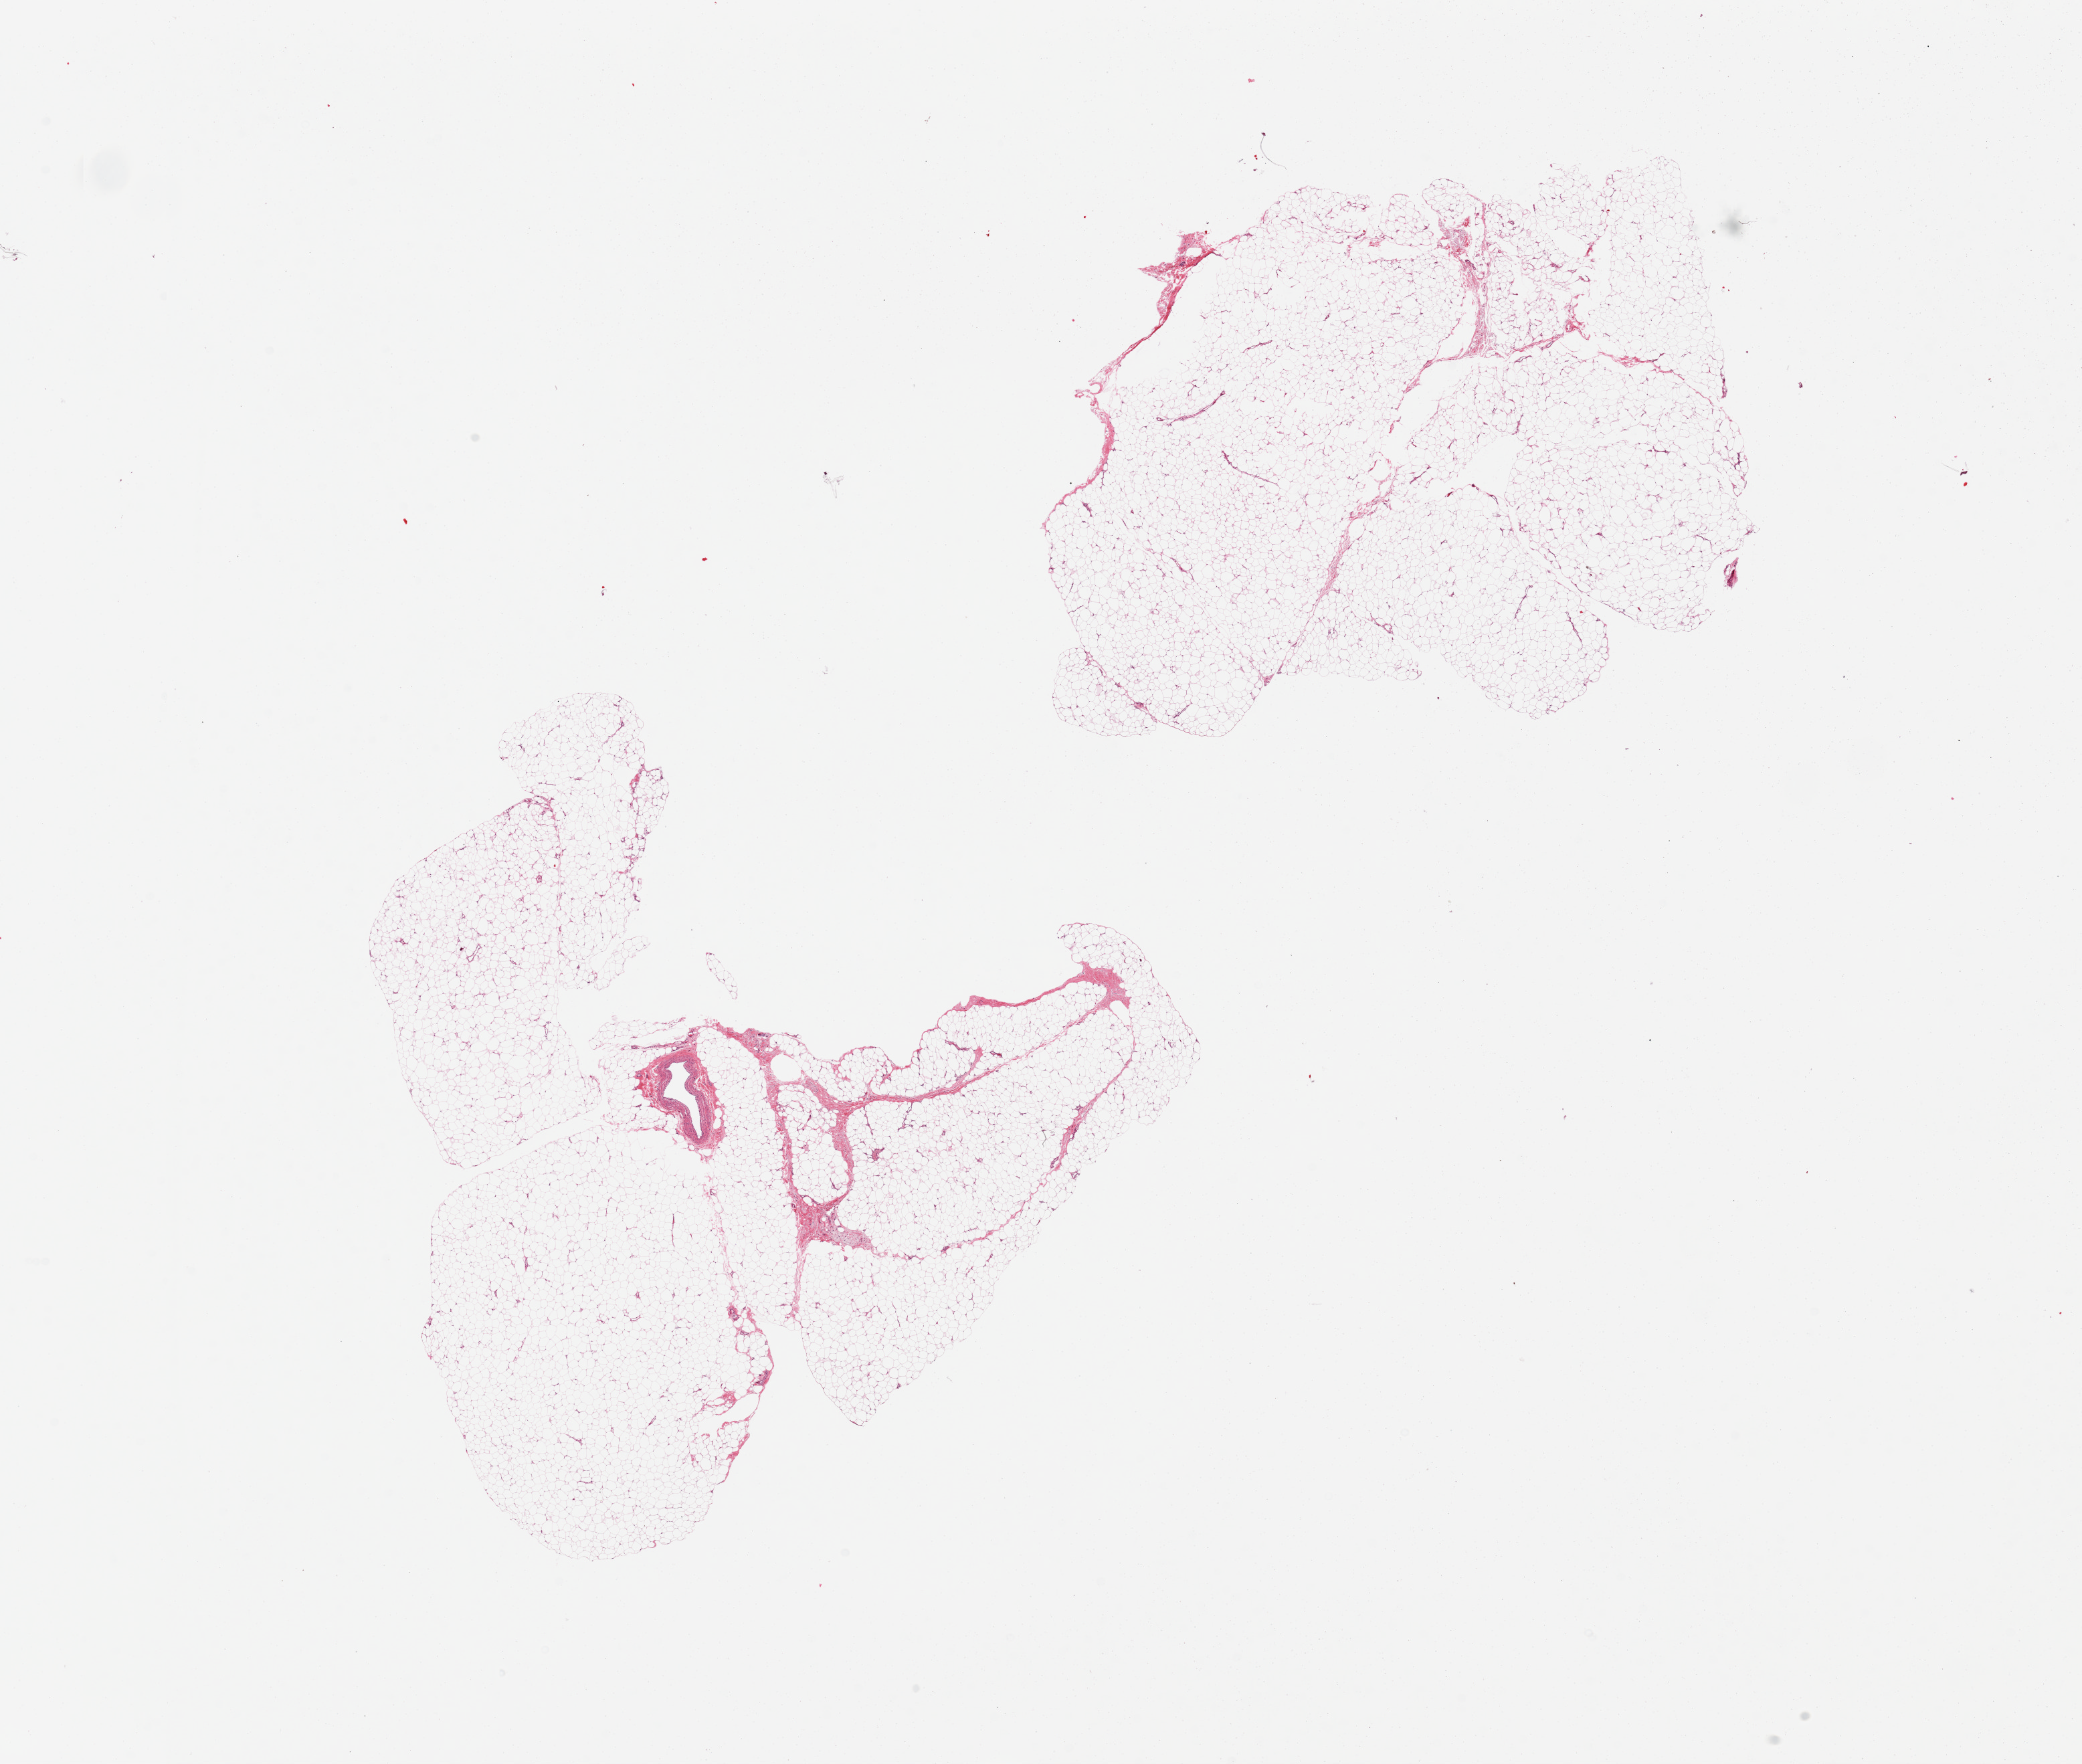
Hematoxylin and eosin (H&E) whole-slide image, brightfield — whole scanned area (about 24.6 x 20.9 mm, acquisition: 20x scan) shown as a low-resolution overview, PAXgene-fixed, paraffin-embedded tissue, section of adipose tissue (target tissue), donor tissue sample. Donor sex: female.
Pathologist's review note for this sample: 2 pieces, minimal vascular tissue.